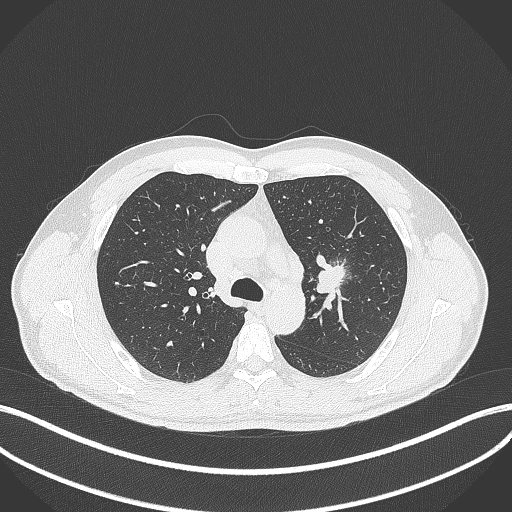
Chest CT, one axial slice; slice 289 of 392 in the series (ordered by position); reconstruction kernel B70f; 120 kVp; lung window (W 1500 / L -600 HU); 1 mm slice thickness; 512 × 512 image matrix. Patient: male, 50 years. Case-level facts recorded for this patient, not image findings: clinical TNM (as recorded): T1c N1 M1b.
Outlined on this slice (bounding box drawn by a radiologist):
- lung tumour (recorded histology: squamous cell carcinoma): bounding box [x1, y1, x2, y2] px = [313, 256, 346, 299]